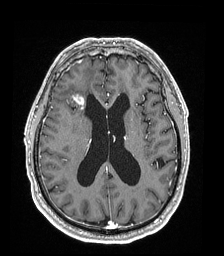
Brain MRI from a brain-tumour surgery series, one axial slice. Position 83 of 192 along the scan axis. T1-weighted post-contrast. 1 mm slice thickness. 224 × 256 image matrix, field of view 224 × 256 mm. Case-level facts recorded for this patient, not image findings: histopathology: Astrocytoma; WHO grade: 4.
Outlined on this slice (outlined manually by an expert reader):
- tumour: bounding box [x1, y1, x2, y2] px = [71, 94, 84, 109]